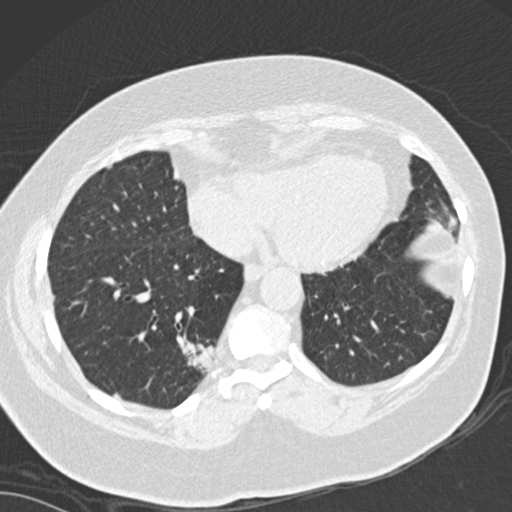
Low-dose screening chest CT, one axial slice. Slice 51 of 162 in the series (ordered by position). 120 kVp. Lung window (W 1500 / L -600 HU). 2 mm slice thickness. 512 × 512 image matrix, field of view 328 × 328 mm.
Outlined on this slice (manually delineated by an expert):
- lesion 1 (tumor, lower lobe of right lung): bounding box <183,340,214,373> (left, top, right, bottom; pixels)